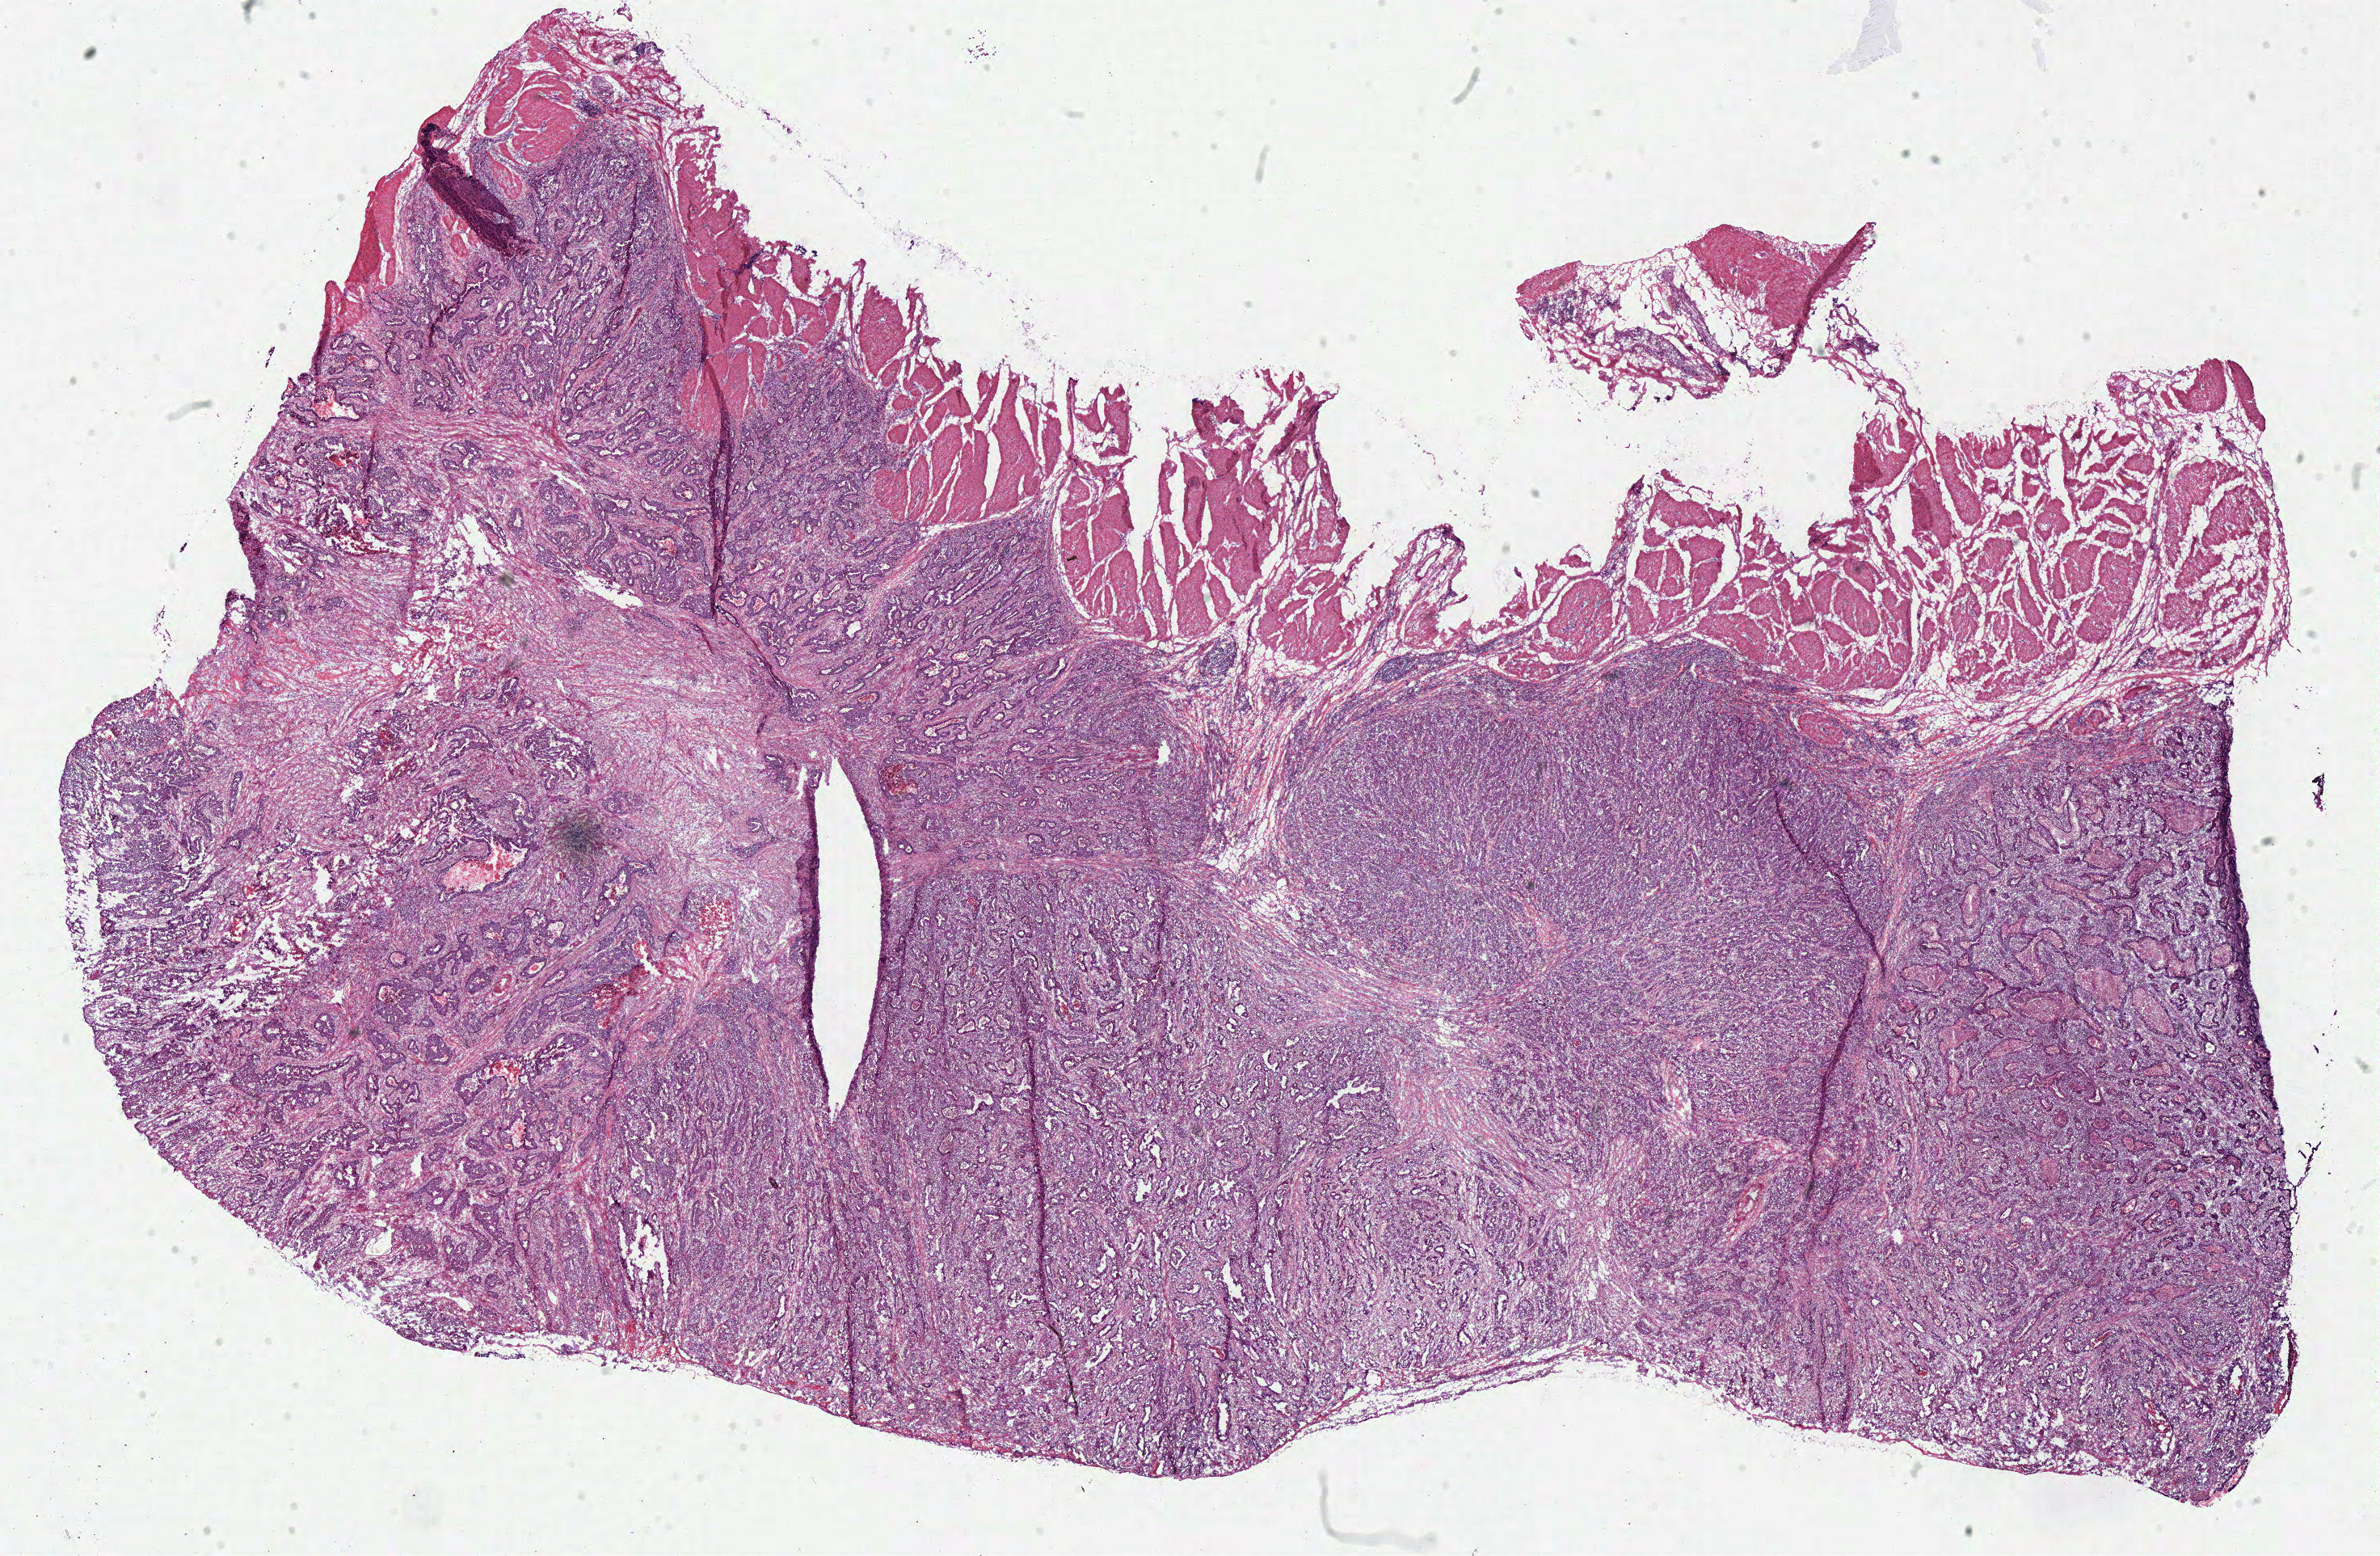
Whole-slide histology image, H&E-stained — whole scanned area (about 23.2 x 15.2 mm, acquisition: 40x scan) shown as a low-resolution overview, frozen section from the bottom of the tissue portion, primary tumour sample from the stomach. Patient: male, age at initial diagnosis 67 years. Histologic grade: G2 (moderately differentiated). Composition of this section per pathologist review: tumour cells 70%, tumour nuclei 75%, normal cells 0%, stromal cells 20%, necrosis 10%.
AJCC pathologic stage: IIB (7th edition). Diagnosis: Adenocarcinoma, NOS (body of stomach).